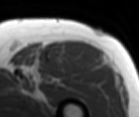
MRI of an extremity soft-tissue mass, one axial slice. Slice 73 of 86 in the series (ordered by position). MR volume resampled by the dataset authors to the PET/CT grid (not the native acquisition matrix). 139 × 117 image matrix, field of view 136 × 114 mm. Male patient. From the clinical record (not read from this slice): histological type: extraskeletal osteosarcoma; grade: high; site of the primary tumour: thigh.
Structures marked on this image (expert contour drawn on MRI and transferred to this co-registered scan by the dataset authors):
- gross tumour volume (mass): box from (x=47, y=41) to (x=103, y=71) px